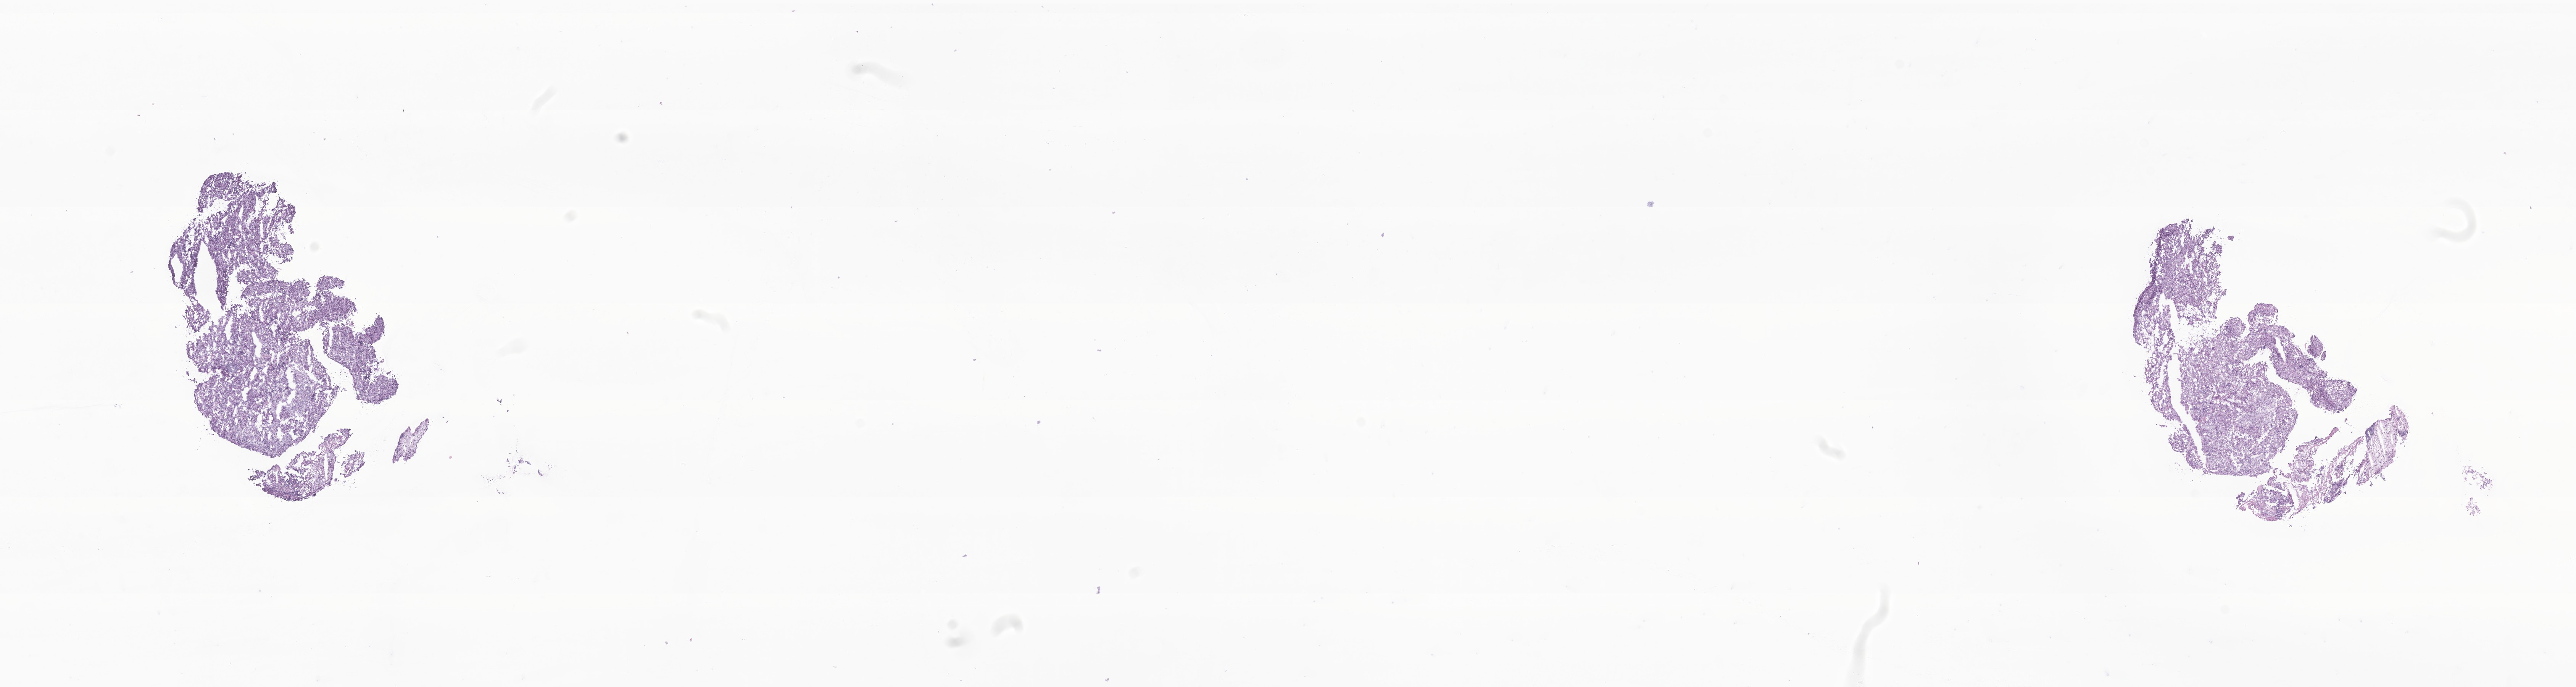
Digitized H&E-stained section of tumor tissue from the nasopharynx, low-resolution overview of the scanned area, about 28.5 x 7.6 mm; frozen section. Patient male; age 212 months (17 years 8 months).
Diagnosis: Carcinoma, NOS.